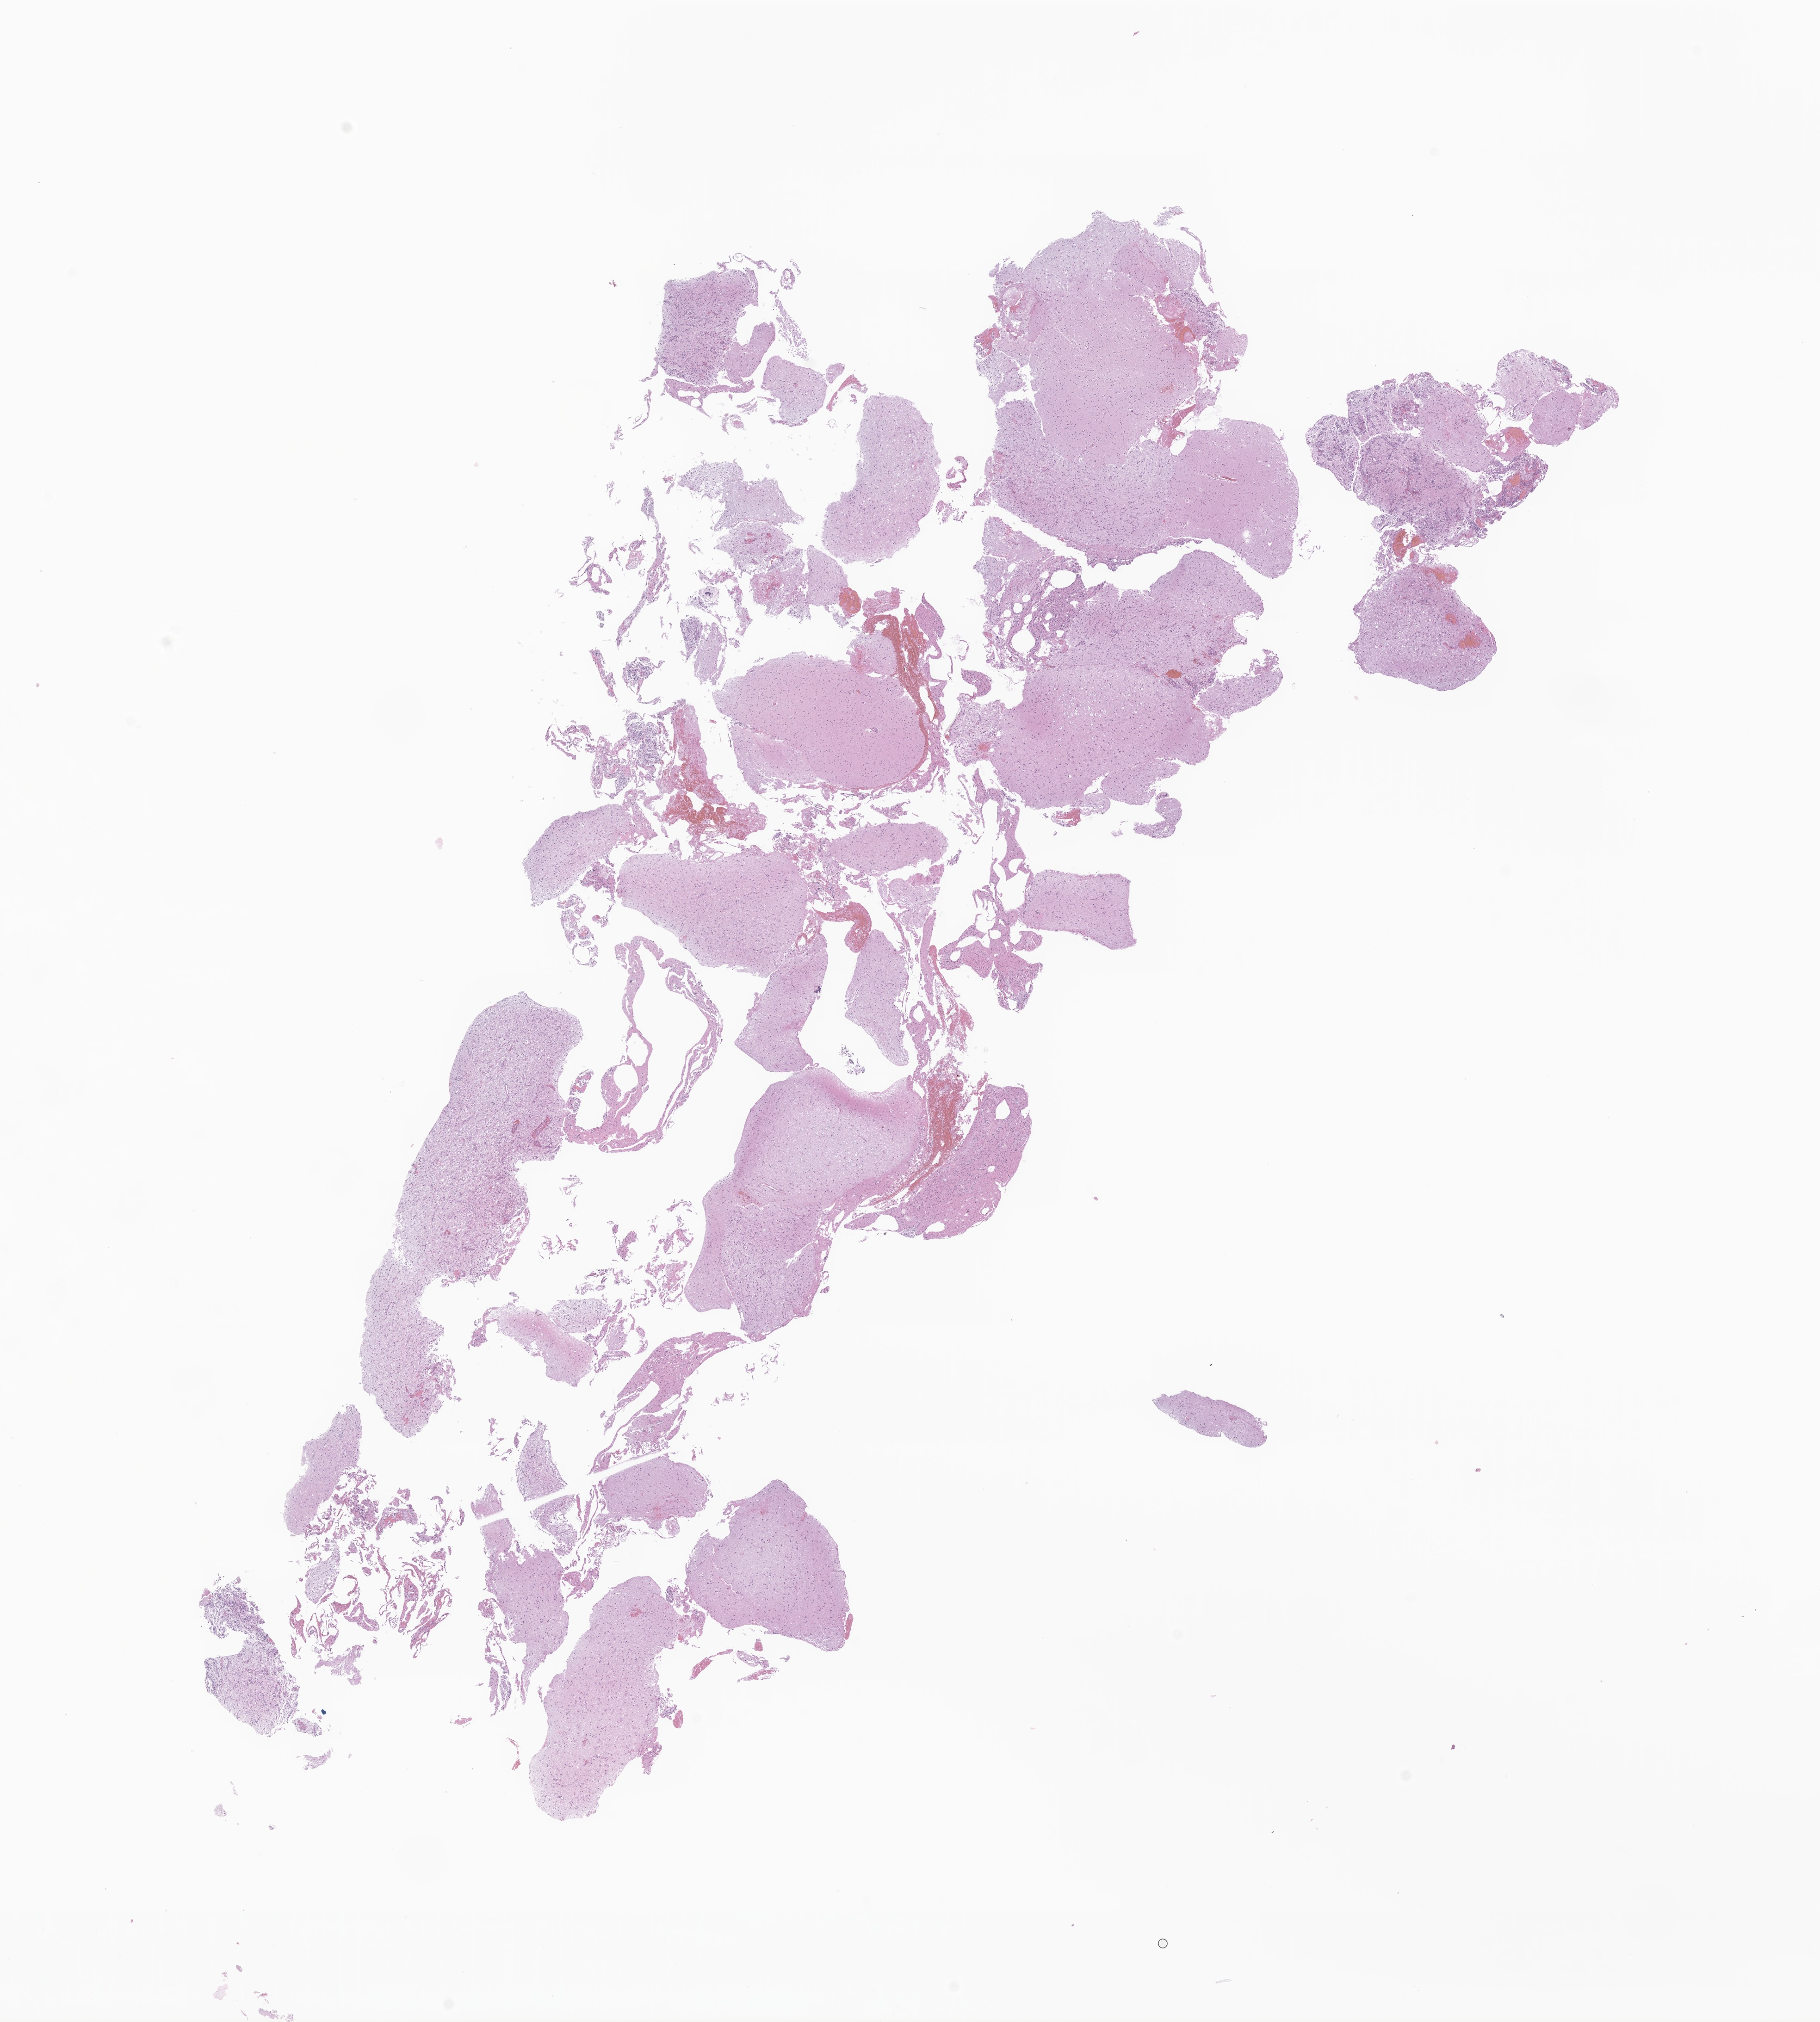
Whole-slide image, haematoxylin and eosin stain of tumor tissue from the temporal lobe, whole scanned area (about 16.6 x 18.4 mm) shown as a low-resolution overview. Formalin-fixed paraffin-embedded section. Male patient, age 141 months.
Diagnosis: Ganglioglioma, NOS.